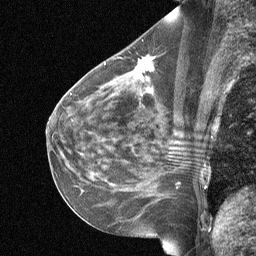
Breast MRI (dynamic contrast-enhanced), one sagittal slice; slice 34 of 64 in the series (ordered by position); dynamic contrast-enhanced study with each time point stored as its own series, time point 2 of 3 at this slice position (early post-contrast, ordered by acquisition time); 1.5 T; TE 4.8 ms, TR 27 ms; 2 mm slice thickness; 256 × 256 image matrix, field of view 200 × 200 mm. Patient: female, 51 years. Case-level facts recorded for this patient, not image findings: setting: breast cancer imaged before/during neoadjuvant chemotherapy; receptor status: HR-positive, HER2-negative.
Annotated regions visible in this slice (semi-automatic segmentation, software-assisted and operator-edited):
- analysis volume of interest (the breast-tissue region the enhancement analysis was run in; not a lesion): bounding box [x1, y1, x2, y2] px = [88, 42, 188, 119]
- tumour enhancement mask (voxels above the 90 % enhancement threshold inside the analysis volume of interest): [134, 57, 153, 91]